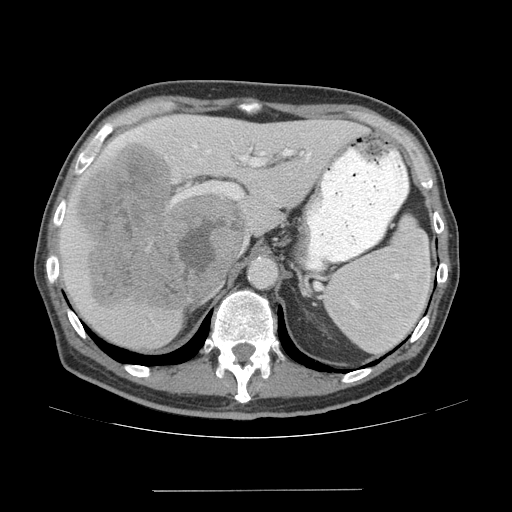
Contrast-enhanced abdominal CT (liver protocol), one axial slice. Position 42 of 77 along the scan axis. Reconstruction kernel STANDARD. 140 kVp. Soft-tissue window (W 400 / L 40 HU). 512 × 512 image matrix, field of view 400 × 400 mm. Case-level facts recorded for this patient, not image findings: diagnosis: hepatocellular carcinoma (patient treated with transarterial chemoembolisation; whether this scan precedes or follows treatment is not stated here); TNM stage (as recorded): Stage-IVA; Child-Pugh class: A; tumour differentiation: well differentiated; tumour nodularity: uninodular.
Outlined on this slice (semi-automatically segmented with operator editing):
- liver parenchyma outside the tumour (the mass and vessels are separate outlines, so this box may not span the whole liver): bounding box (x1, y1, x2, y2) in pixels: (60, 114, 364, 348)
- mass: (76, 142, 248, 310)
- liver vessels: (106, 125, 310, 203)